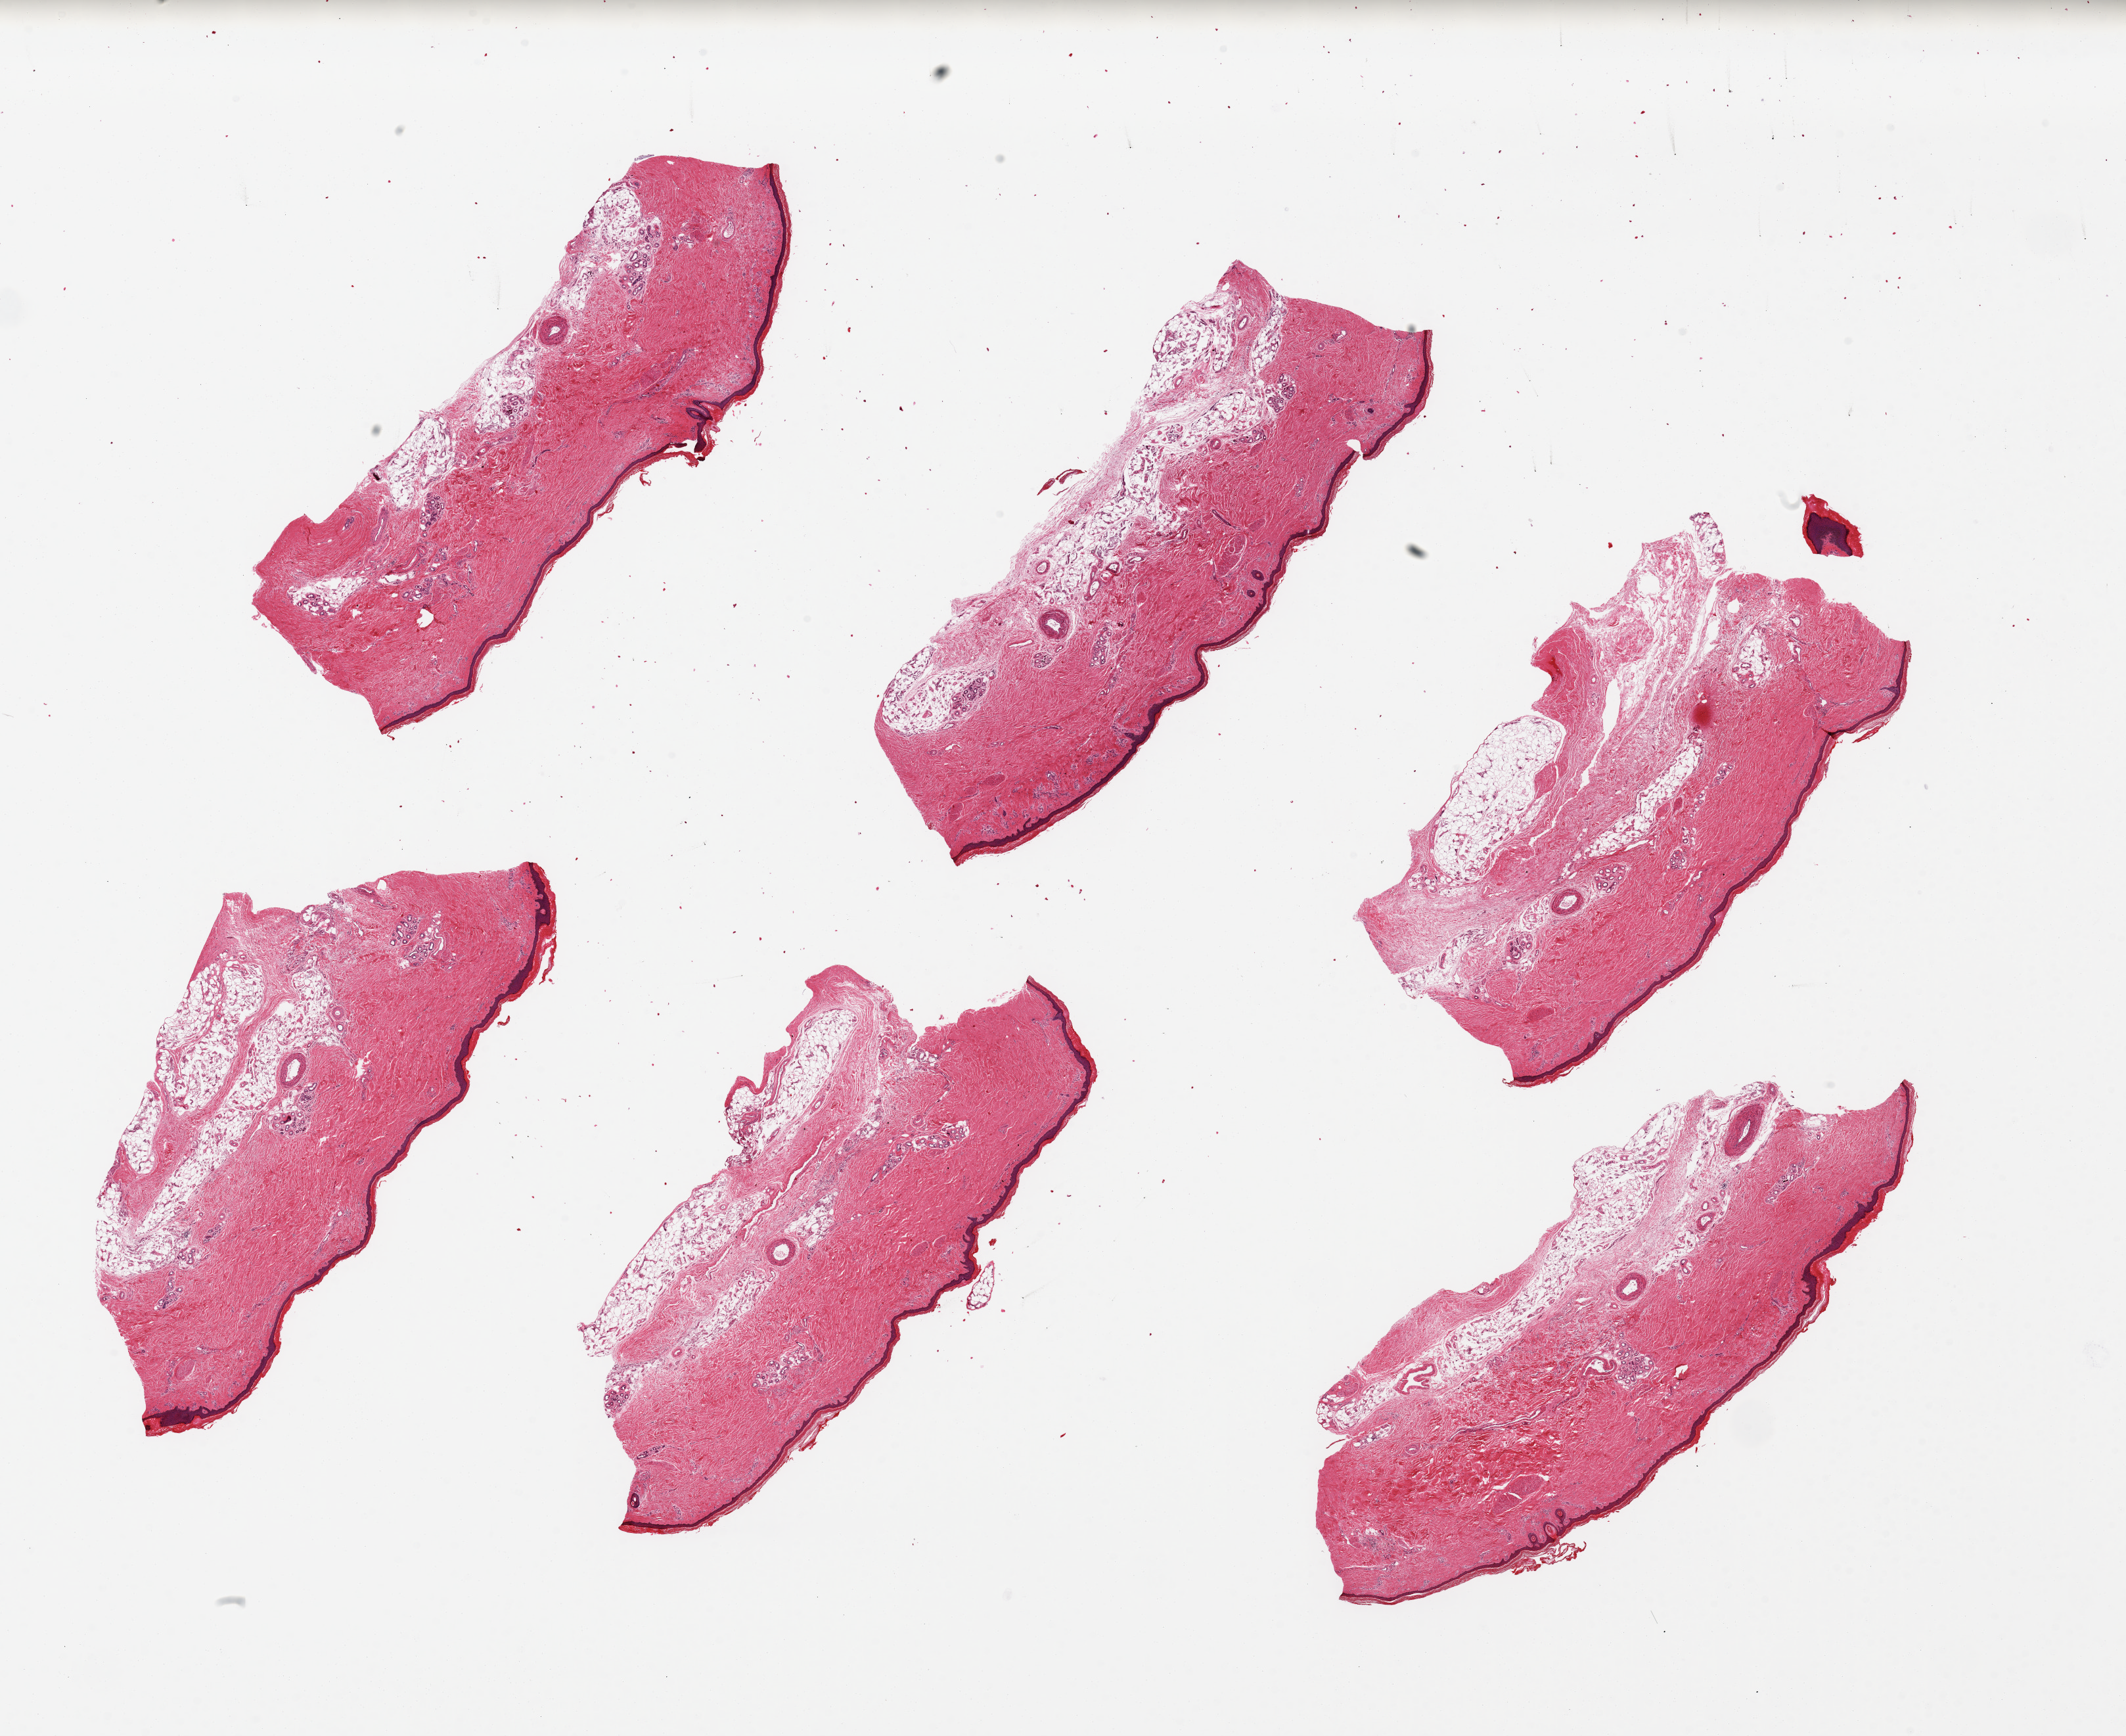
Whole-slide image, H&E stain, brightfield, shown as a low-resolution overview of the whole scanned area (about 25.6 x 20.9 mm, from a 20x scan); PAXgene-fixed paraffin-embedded (PFPE) section; target tissue: skin of lower leg; donor tissue sample. Donor sex: male.
Review note (as recorded): 6 pieces ~7.5x3mm. Squamous epithelium is ~2-3% of thickness.